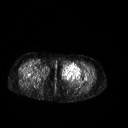
FDG PET of an extremity soft-tissue mass (from a PET/CT study), one axial slice; slice 248 of 267 in the series (ordered by position); 3.27 mm slice thickness; 128 × 128 image matrix, field of view 500 × 500 mm. Female patient, age 42 years. Case-level facts recorded for this patient, not image findings: histological type: pleiomorphic leiomyosarcoma; grade: intermediate; site of the primary tumour: left thigh.
Outlined on this slice (expert contour drawn on MRI and transferred to this co-registered scan by the dataset authors):
- gross tumour volume including surrounding oedema: bounding box <60,63,82,81> (left, top, right, bottom; pixels)
- gross tumour volume (mass): <60,63,82,81>